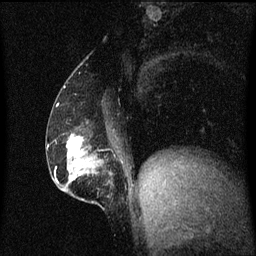
Breast MRI (dynamic contrast-enhanced), one sagittal slice; position 25 of 60 along the scan axis; dynamic contrast-enhanced series, image 2 of 3 at this slice position (ordered by acquisition); 1.5 T; TE 4.2 ms, TR 8.4 ms; 2 mm slice thickness; 256 × 256 image matrix. Female patient, age 52 years. Case-level facts recorded for this patient, not image findings: setting: breast cancer imaged before/during neoadjuvant chemotherapy; receptor status: HER2-positive.
Annotated regions visible in this slice (semi-automatically segmented with operator editing):
- analysis volume of interest (the breast-tissue region the enhancement analysis was run in; not a lesion): bounding box (x1, y1, x2, y2) in pixels: (62, 134, 113, 203)
- tumour enhancement mask (voxels above the 70 % enhancement threshold inside the analysis volume of interest): (68, 136, 82, 163)